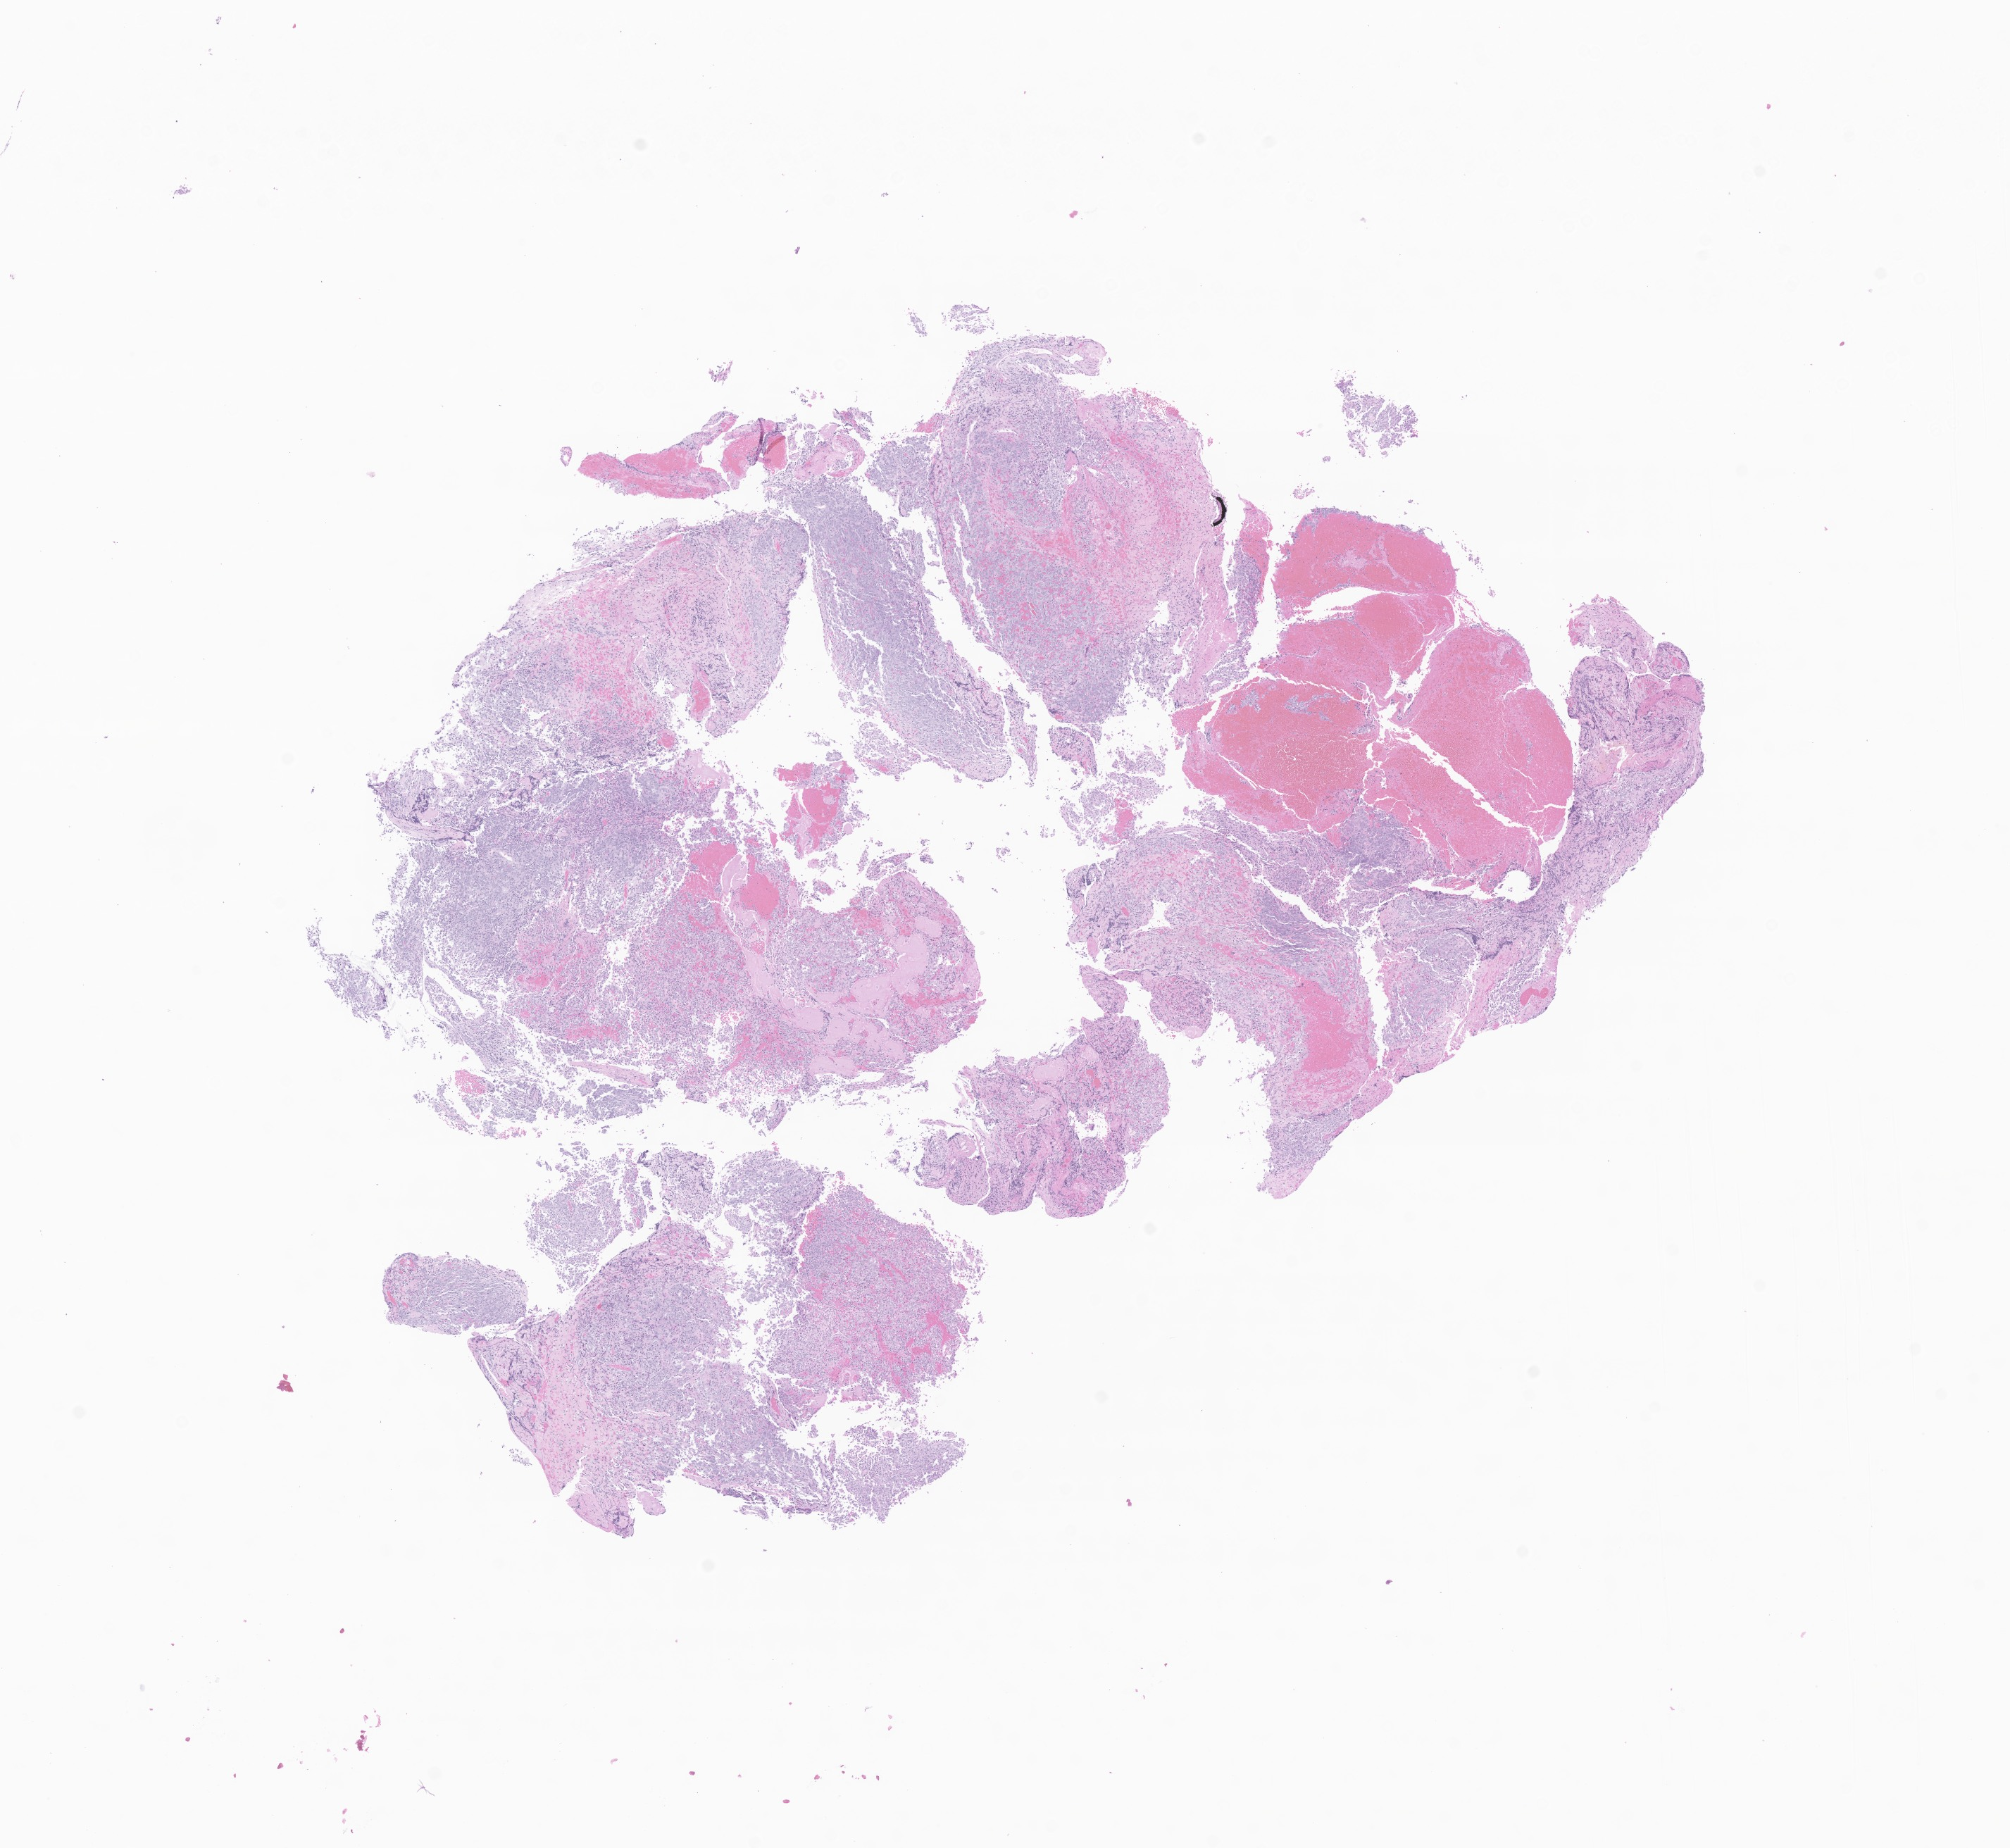
Whole-slide image, haematoxylin and eosin stain of tumor tissue from the spinal cord, low-resolution overview of the scanned area, about 12.0 x 11.1 mm, FFPE section. Patient: male, age 77 months (6 years 5 months).
Diagnosis (ICD-O-3 morphology term): Atypical teratoid/rhabdoid tumor.